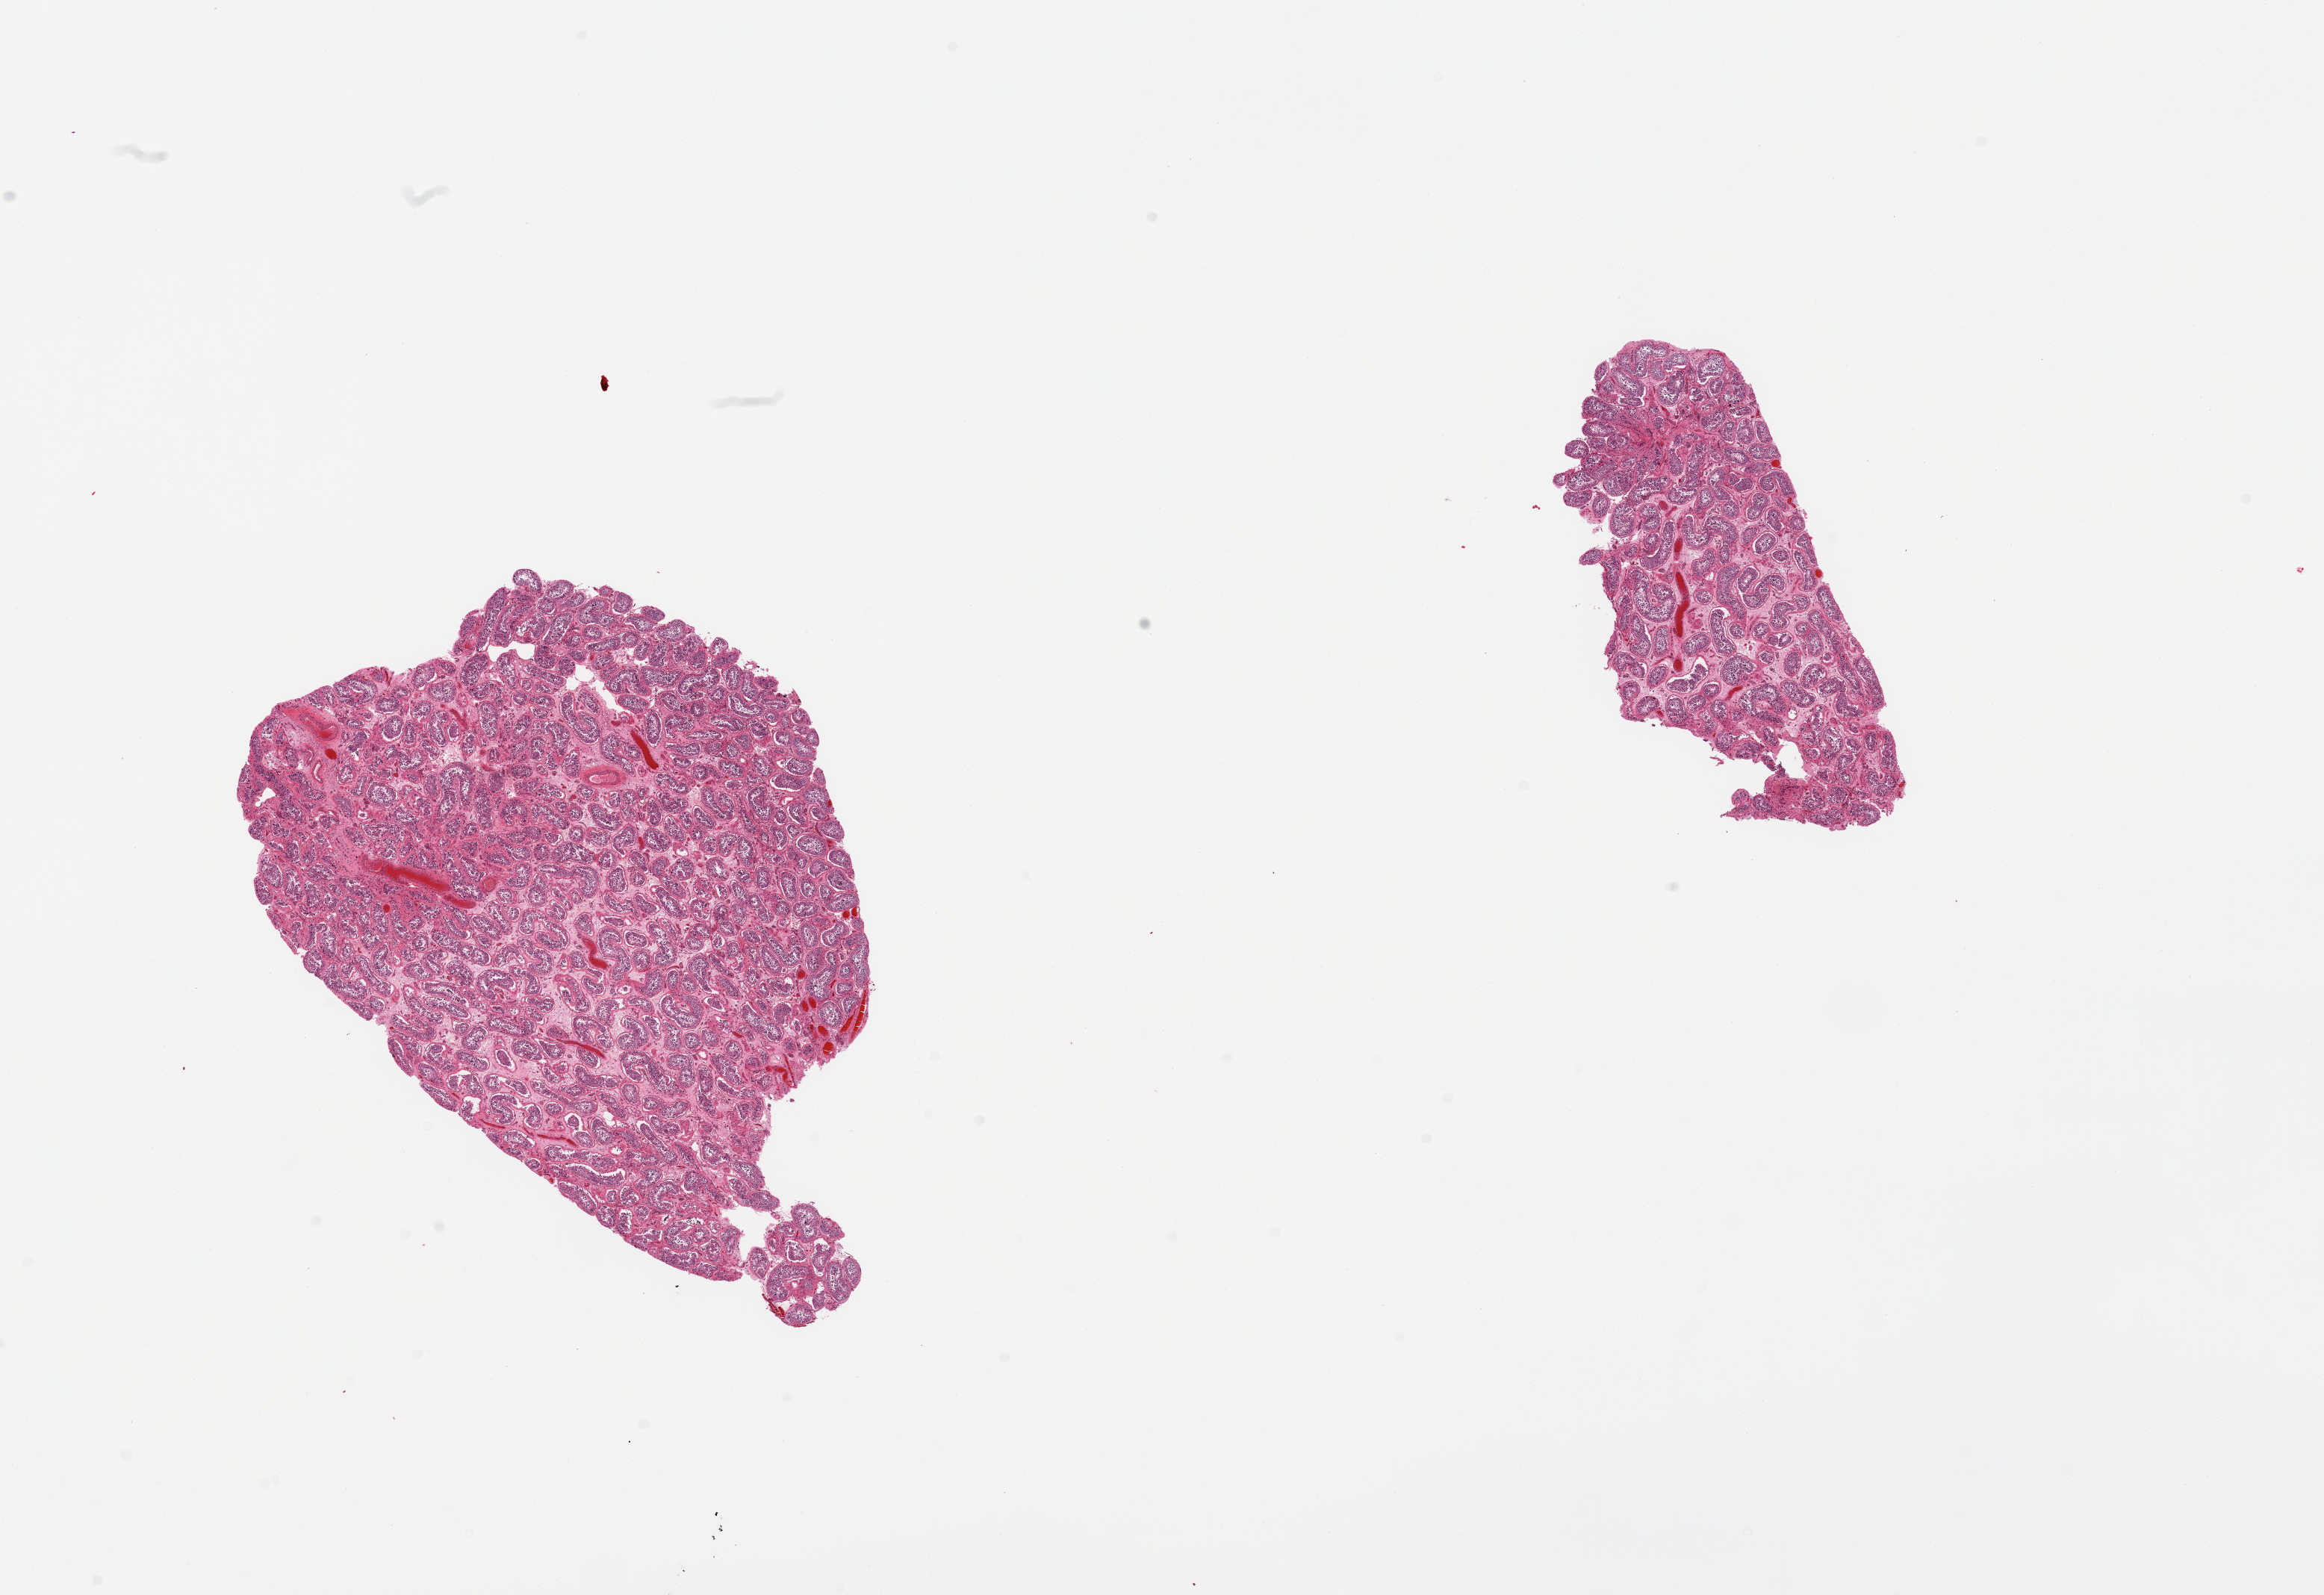
Digitized H&E-stained section, a low-resolution overview of the entire scanned area, about 24.6 x 16.9 mm (slide scanned at 20x); PAXgene-fixed paraffin-embedded (PFPE) section; target tissue: testis; donor tissue sample. Donor: male.
Review note (as recorded): 2 pieces; spermatogenesis present but appears redueced.